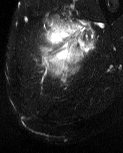
MRI of an extremity soft-tissue mass, one axial slice. Slice 12 of 60 in the series (ordered by position). T2-weighted fat-saturated. MR volume resampled by the dataset authors to the PET/CT grid (not the native acquisition matrix). 3.27 mm slice thickness. 123 × 153 image matrix. Male patient. From the clinical record (not read from this slice): histological type: pleiomorphic liposarcoma; grade: high; site of the primary tumour: left thigh.
Outlined on this slice (expert contour drawn on MRI and transferred to this co-registered scan by the dataset authors):
- gross tumour volume including surrounding oedema: box from (x=43, y=15) to (x=96, y=82) px